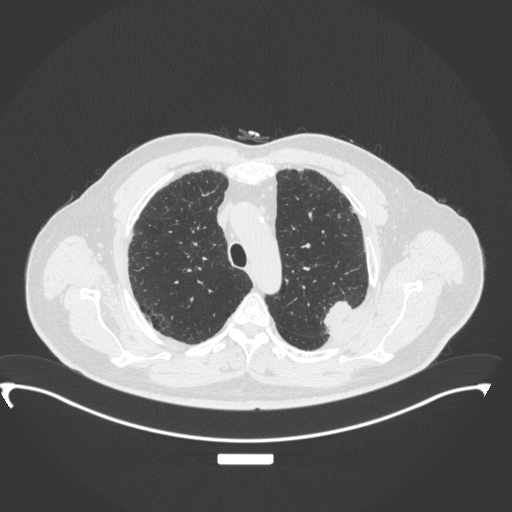
Chest CT, one axial slice. Position 276 of 350 along the scan axis. Lung window (W 1500 / L -600 HU). 1 mm slice thickness. 512 × 512 image matrix, field of view 459 × 459 mm. Male patient, age 64 years. Case-level facts recorded for this patient, not image findings: clinical TNM (as recorded): T1c N1 M1.
Outlined on this slice (rectangle marked by the reading radiologist):
- lung tumour (recorded histology: adenocarcinoma): bounding box [x1, y1, x2, y2] px = [320, 297, 357, 334]